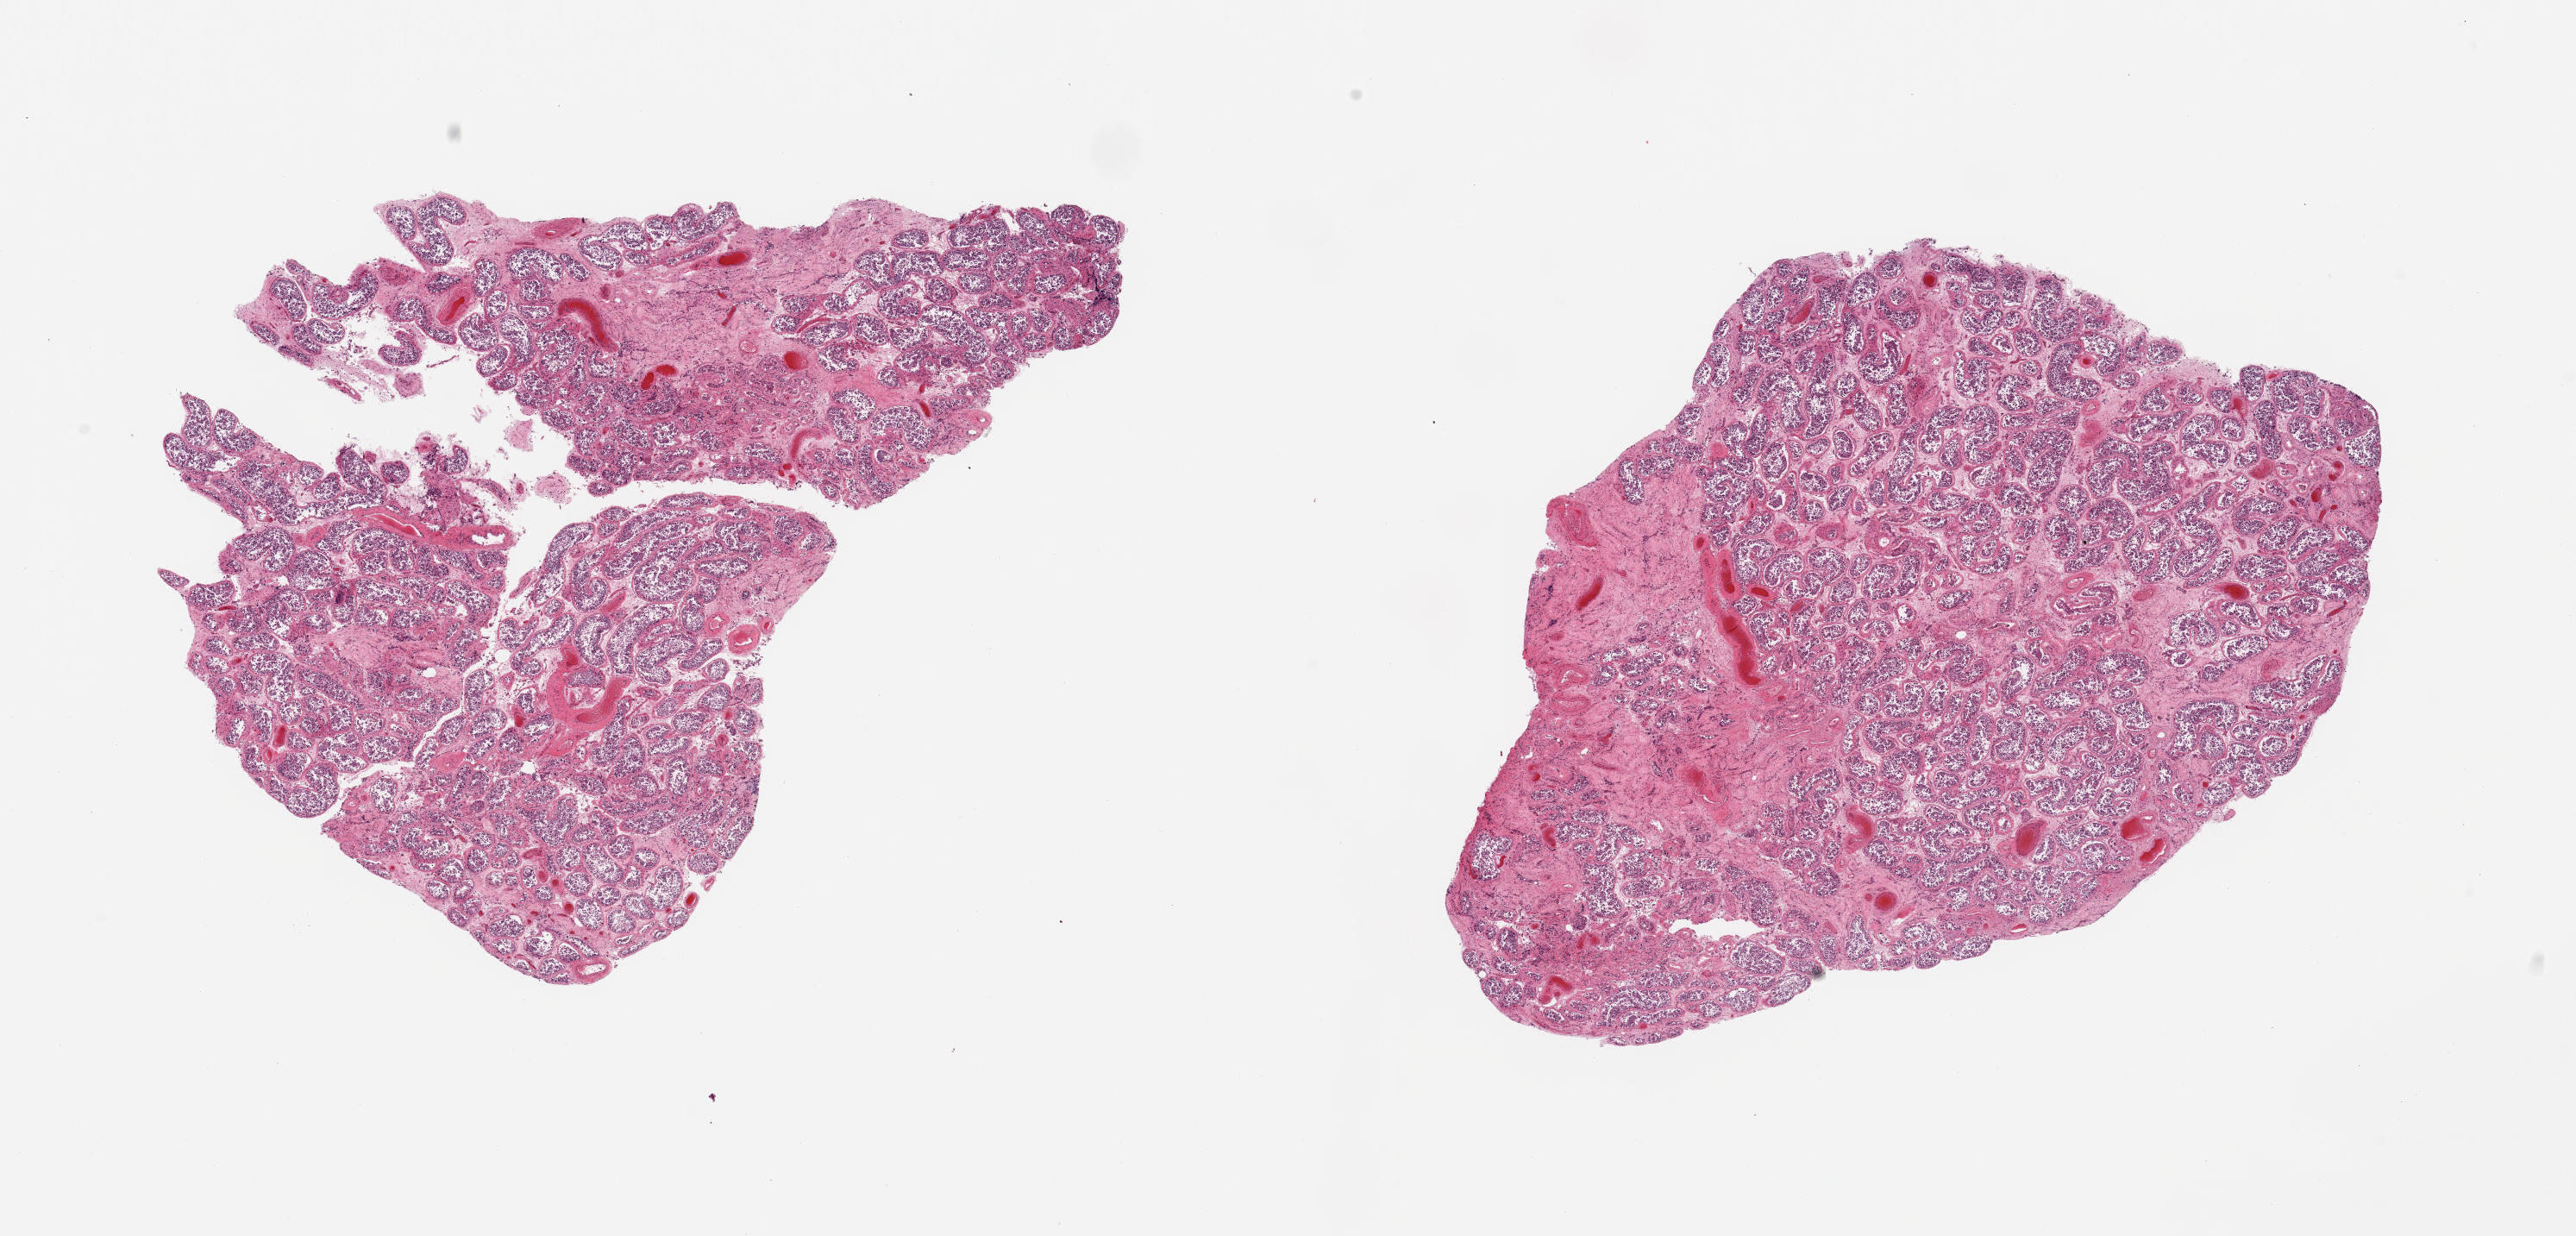
Haematoxylin and eosin whole-slide image, brightfield — shown as a low-resolution overview of the whole scanned area (about 23.6 x 11.3 mm, from a 20x scan). PAXgene-fixed paraffin-embedded (PFPE) section. Target tissue: testis. Donor tissue sample.
Review note (as recorded): 2 pieces; reduced spermatic maturation; parenchymal sclerosis occupies 30 & 10%.